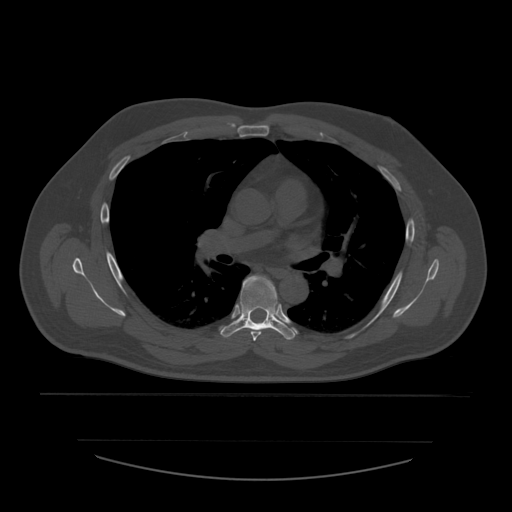
CT including the spine, one axial slice; slice 384 of 532 in the series (ordered by position); reconstruction kernel STANDARD; 120 kVp; bone window (W 1800 / L 400 HU); 1.25 mm slice thickness; 512 × 512 image matrix, field of view 441 × 441 mm. Patient age 44 years. Case-level facts recorded for this patient, not image findings: primary cancer: soft tissue sarcoma.
Outlined on this slice (semi-automatically segmented with operator editing):
- T5 vertebra: box from (x=251, y=276) to (x=274, y=341) px
- T6 vertebra: (x=221, y=275)–(x=298, y=340)